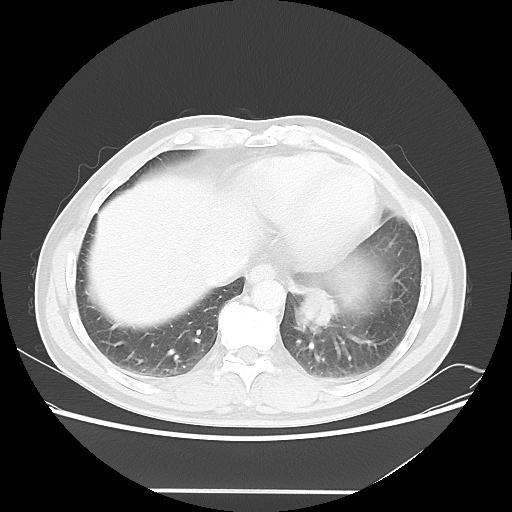
Chest CT, one axial slice; slice 14 of 53 in the series (ordered by position); reconstruction kernel LUNG; 120 kVp; lung window (W 1500 / L -600 HU); 5 mm slice thickness; 512 × 512 image matrix, field of view 385 × 385 mm. Patient: male, 61 years. Case-level facts recorded for this patient, not image findings: clinical TNM (as recorded): T1c N0 M0.
Structures marked on this image (rectangle marked by the reading radiologist):
- lung tumour (recorded histology: adenocarcinoma): bounding box [x1, y1, x2, y2] px = [294, 285, 340, 335]